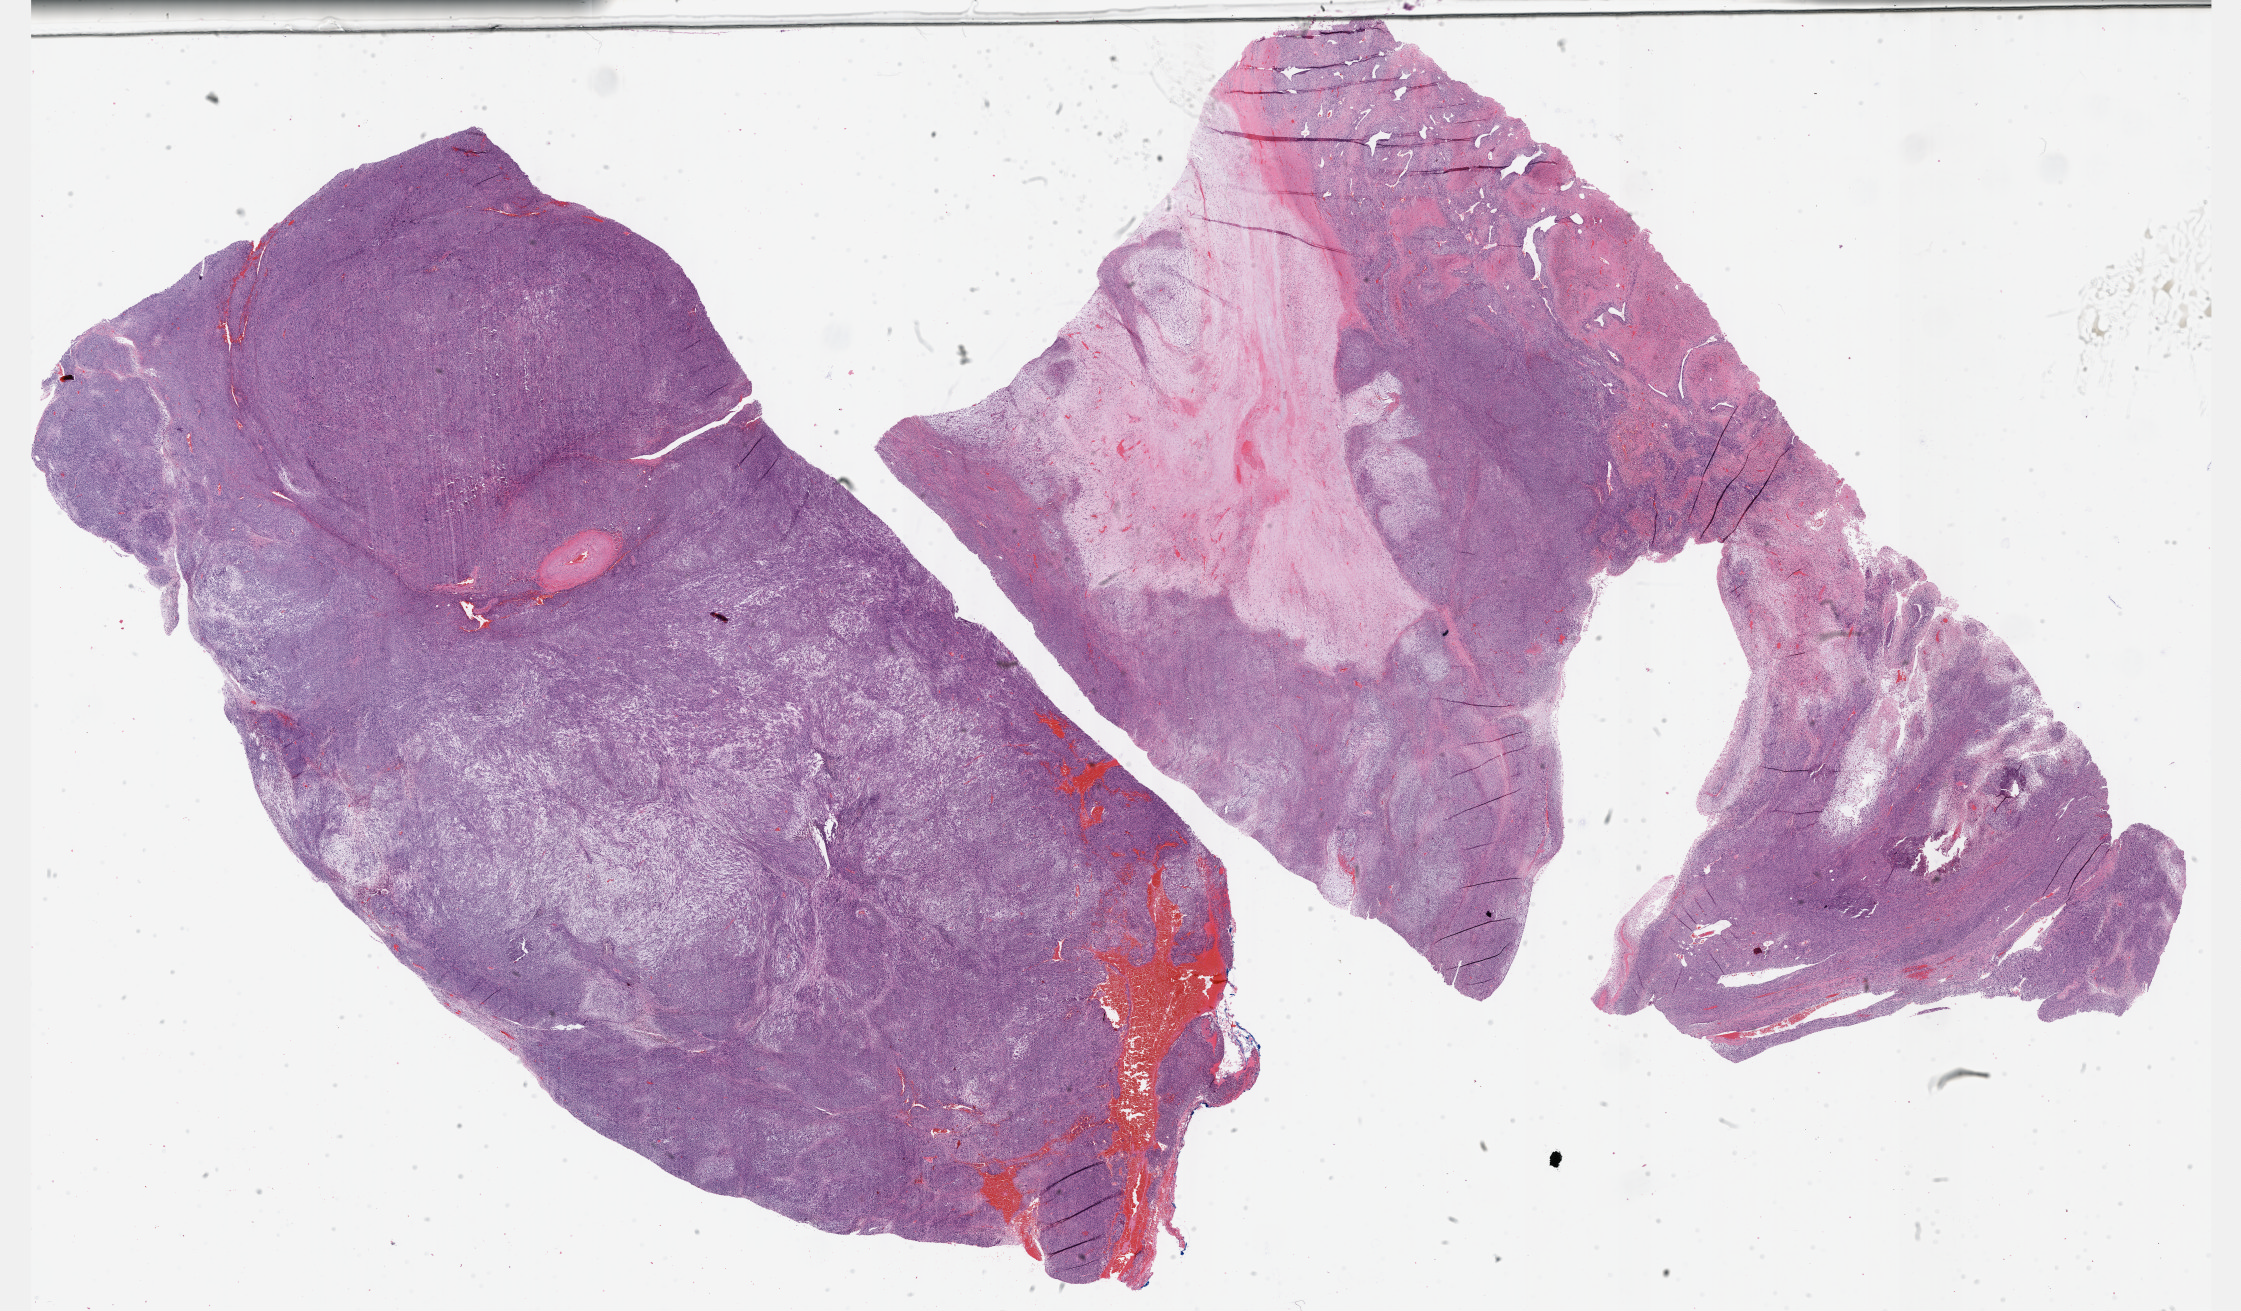
Whole-slide histology image, H&E — a low-resolution overview of the entire scanned area, about 36.2 x 21.2 mm (from a 40x scan); formalin-fixed paraffin-embedded (FFPE) diagnostic section; sample: primary tumour, connective, subcutaneous and other soft tissues. Female patient; age at initial diagnosis 70 years.
Histologic diagnosis: Undifferentiated sarcoma.